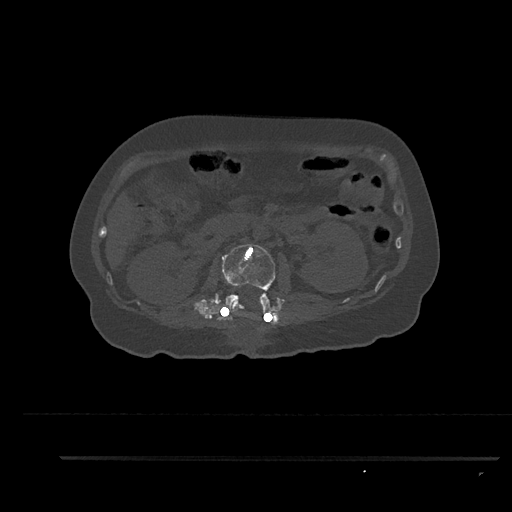
CT including the spine, one axial slice. Slice 181 of 797 in the series (ordered by position). 120 kVp. Bone window (W 1800 / L 400 HU). 0.5 mm slice thickness. 512 × 512 image matrix. Female patient, age 44 years. Case-level facts recorded for this patient, not image findings: primary cancer: renal.
Structures marked on this image (semi-automatically segmented with operator editing):
- L2 vertebra: bounding box (x1, y1, x2, y2) in pixels: (223, 243, 276, 321)